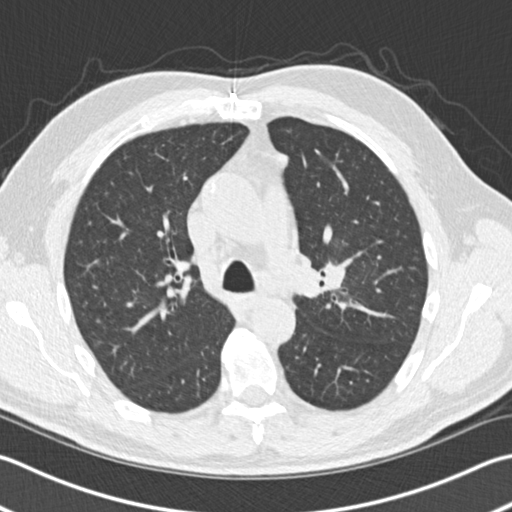
Low-dose screening chest CT, axial slice. Third screening round (two years after baseline). Lung window (W 1500 / L -600 HU). Standard (soft-tissue) reconstruction kernel (B30f). 120 kVp. Slice 52 of 153 in the series. 512 × 512 image matrix. Male participant, aged 65 years at enrolment. Former smoker at enrolment.
Expert reader's lesion annotation, bounding box <307,238,371,303> (left, top, right, bottom; pixels). The screening reader recorded 4 non-calcified nodules or masses ≥4 mm on this exam (left upper lobe, left upper lobe, left lower lobe, right middle lobe); which of them this box marks is not recorded. Participant outcome: lung cancer diagnosed 196 days after this screen — acinar cell carcinoma, left upper lobe, stage IA (AJCC 6th edition), 25 mm at pathology.